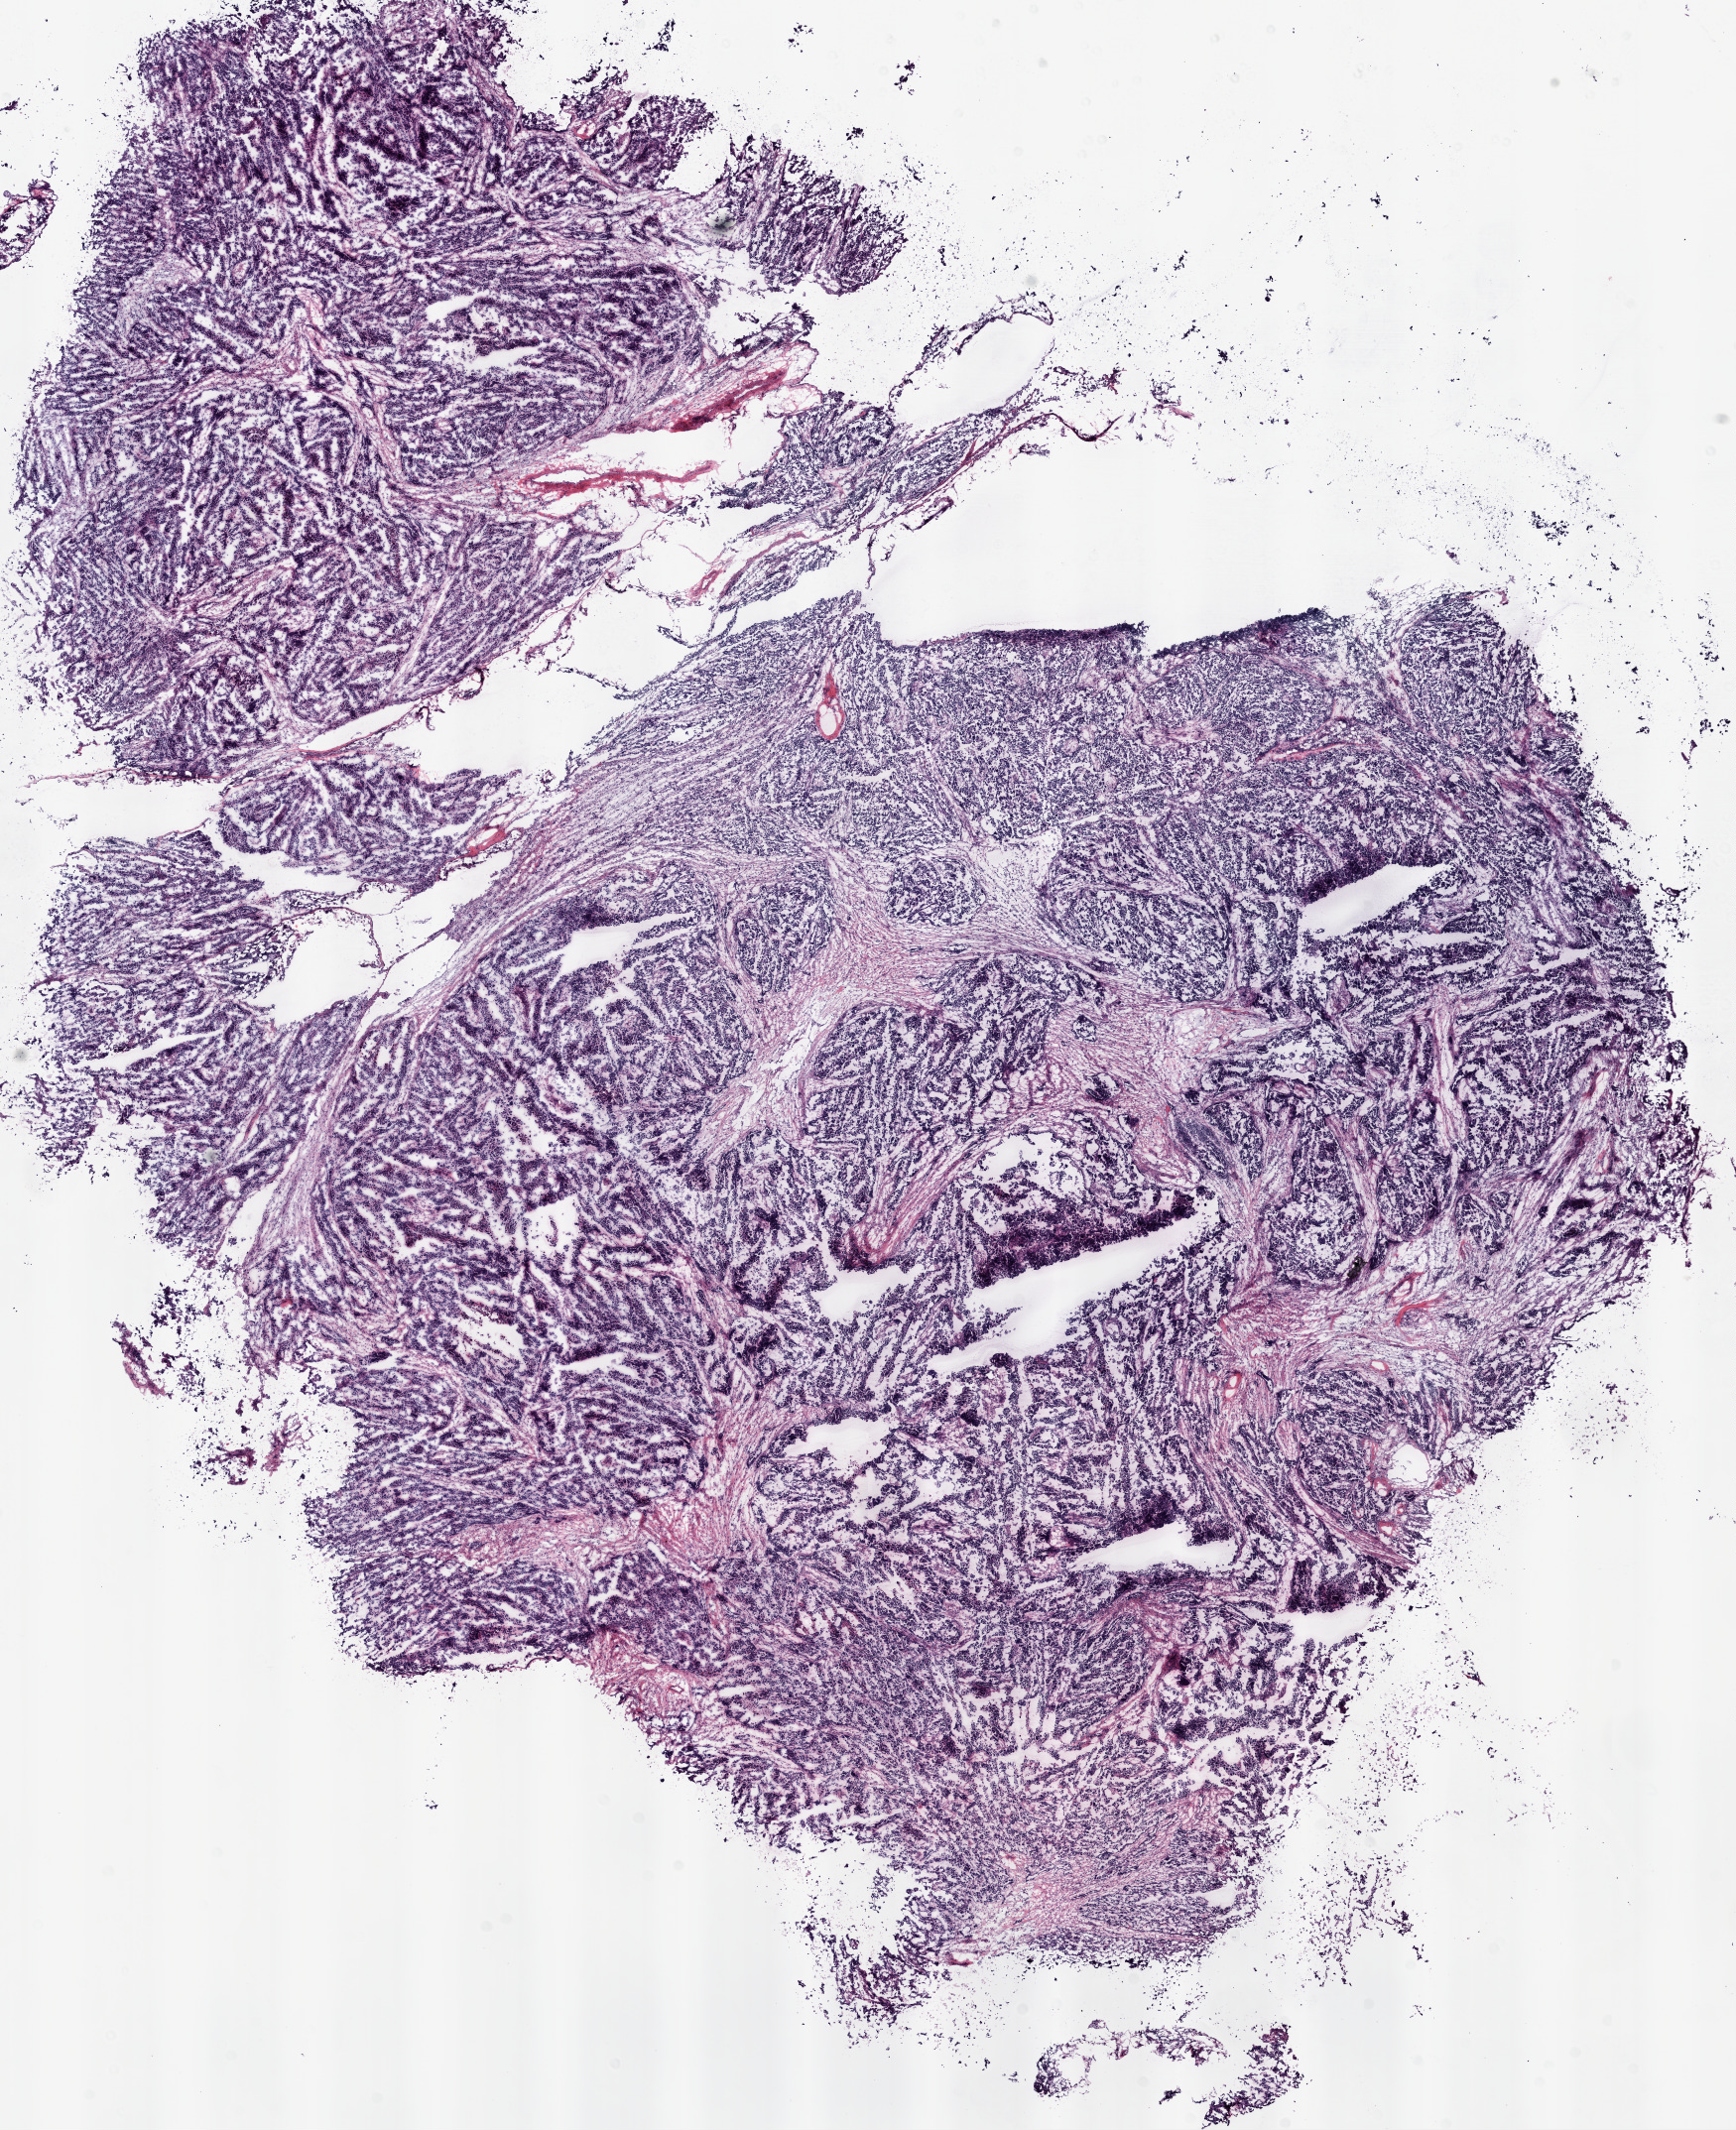
Digitized Hematoxylin and eosin (H&E) stained tissue section (whole slide) — shown as a low-resolution overview of the whole scanned area (about 14.0 x 17.2 mm); frozen section from the top of the tissue portion; primary tumour sample from the ovary. Female patient; age at initial diagnosis 57 years. Histologic grade: GX (grade cannot be assessed). Slide review estimates, as recorded: tumour cells 95%, tumour nuclei 95%, normal cells 0%, stromal cells 5%, necrosis 0%.
Diagnosis: Serous cystadenocarcinoma, NOS. FIGO stage: IV. Laterality: bilateral.